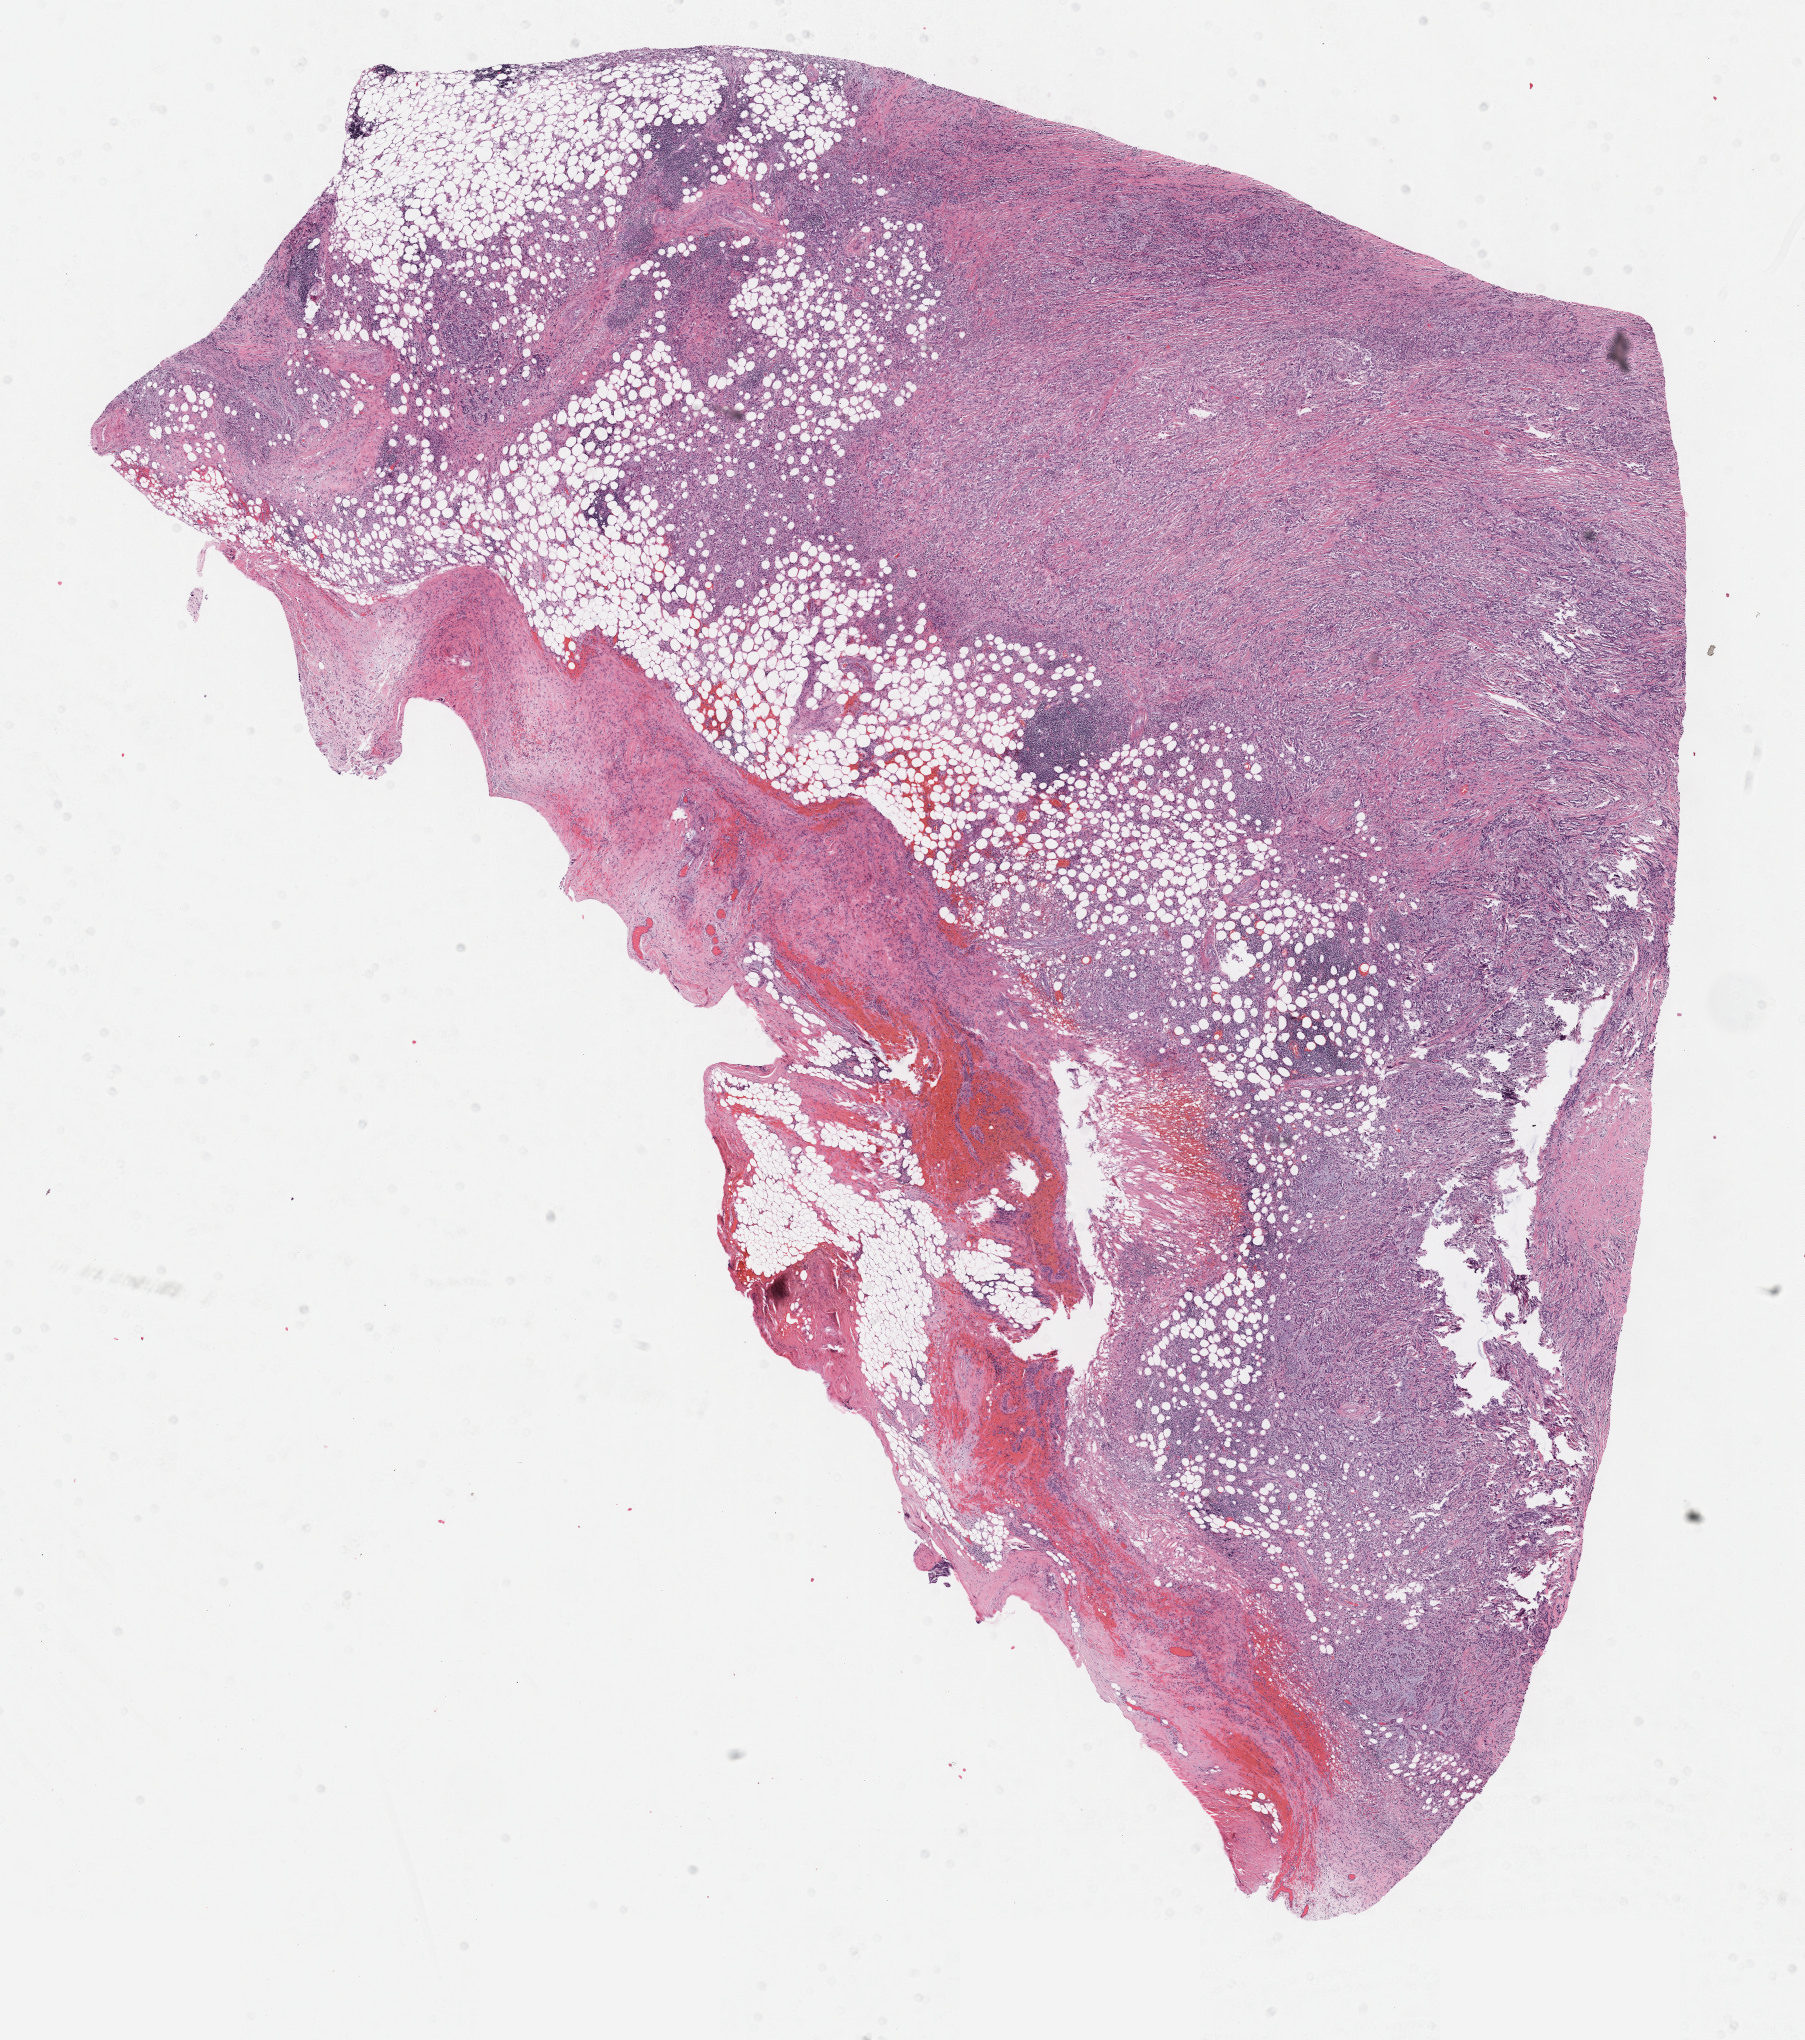
H&E whole-slide image — shown as a low-resolution overview of the whole scanned area (about 14.6 x 16.5 mm, slide scanned at 40x); FFPE section; sample: primary tumour, mesothelium. Patient: male, age at initial diagnosis 61 years.
- laterality: left
- pathologic diagnosis: Epithelioid mesothelioma, malignant (pleura, NOS)
- AJCC pathologic stage: III